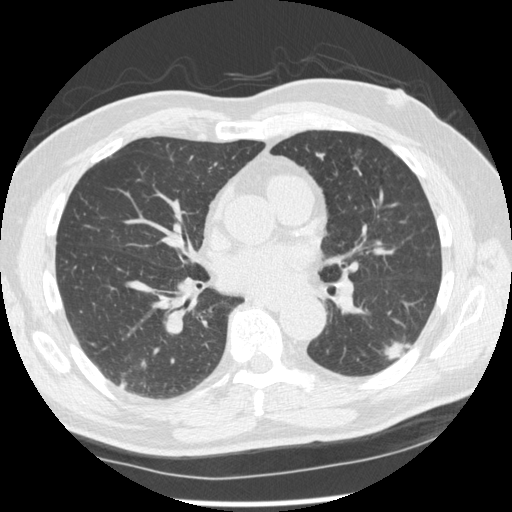
Chest CT (low-dose screening protocol), one axial image; second screening round (one year after baseline); lung window (W 1500 / L -600 HU); standard (soft-tissue) reconstruction kernel (STANDARD); slice 126 of 227 in the series. Male, age 74 years at enrolment. Former smoker at enrolment.
• Lesion marked by an expert reader, bounding box [x1, y1, x2, y2] px = [365, 312, 425, 368].
• The screening reader recorded 7 non-calcified nodules or masses ≥4 mm on this exam; which of them this box marks is not recorded.
• Participant outcome: lung cancer diagnosed 43 days after this screen — squamous cell carcinoma, NOS, left lower lobe, well differentiated (G1), stage IA (AJCC 6th edition), 28 mm at pathology.